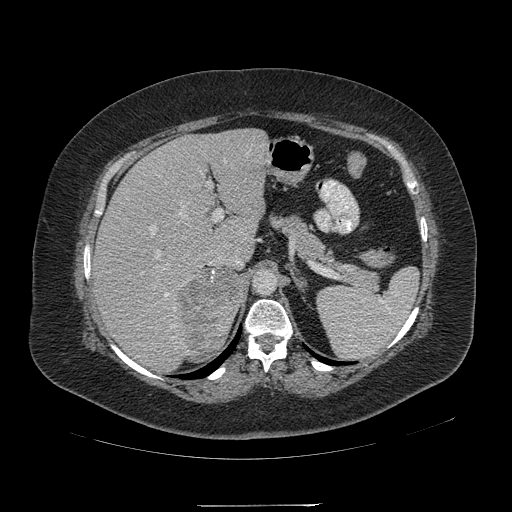
Contrast-enhanced abdominal CT, one axial slice. Slice 144 of 217 in the series (ordered by position). 120 kVp. Intravenous contrast given. Soft-tissue window (W 400 / L 40 HU). 512 × 512 image matrix, field of view 453 × 453 mm. Female patient, age 55 years. Case-level facts recorded for this patient, not image findings: diagnosis: adrenocortical carcinoma; tumour side: right adrenal; tumour size at pathology: 11 cm; Ki-67 index: 20 %; stage (as recorded): 2.
Annotated regions visible in this slice (semi-automatically segmented with operator editing):
- mass: bounding box (x1, y1, x2, y2) in pixels: (178, 269, 242, 358)